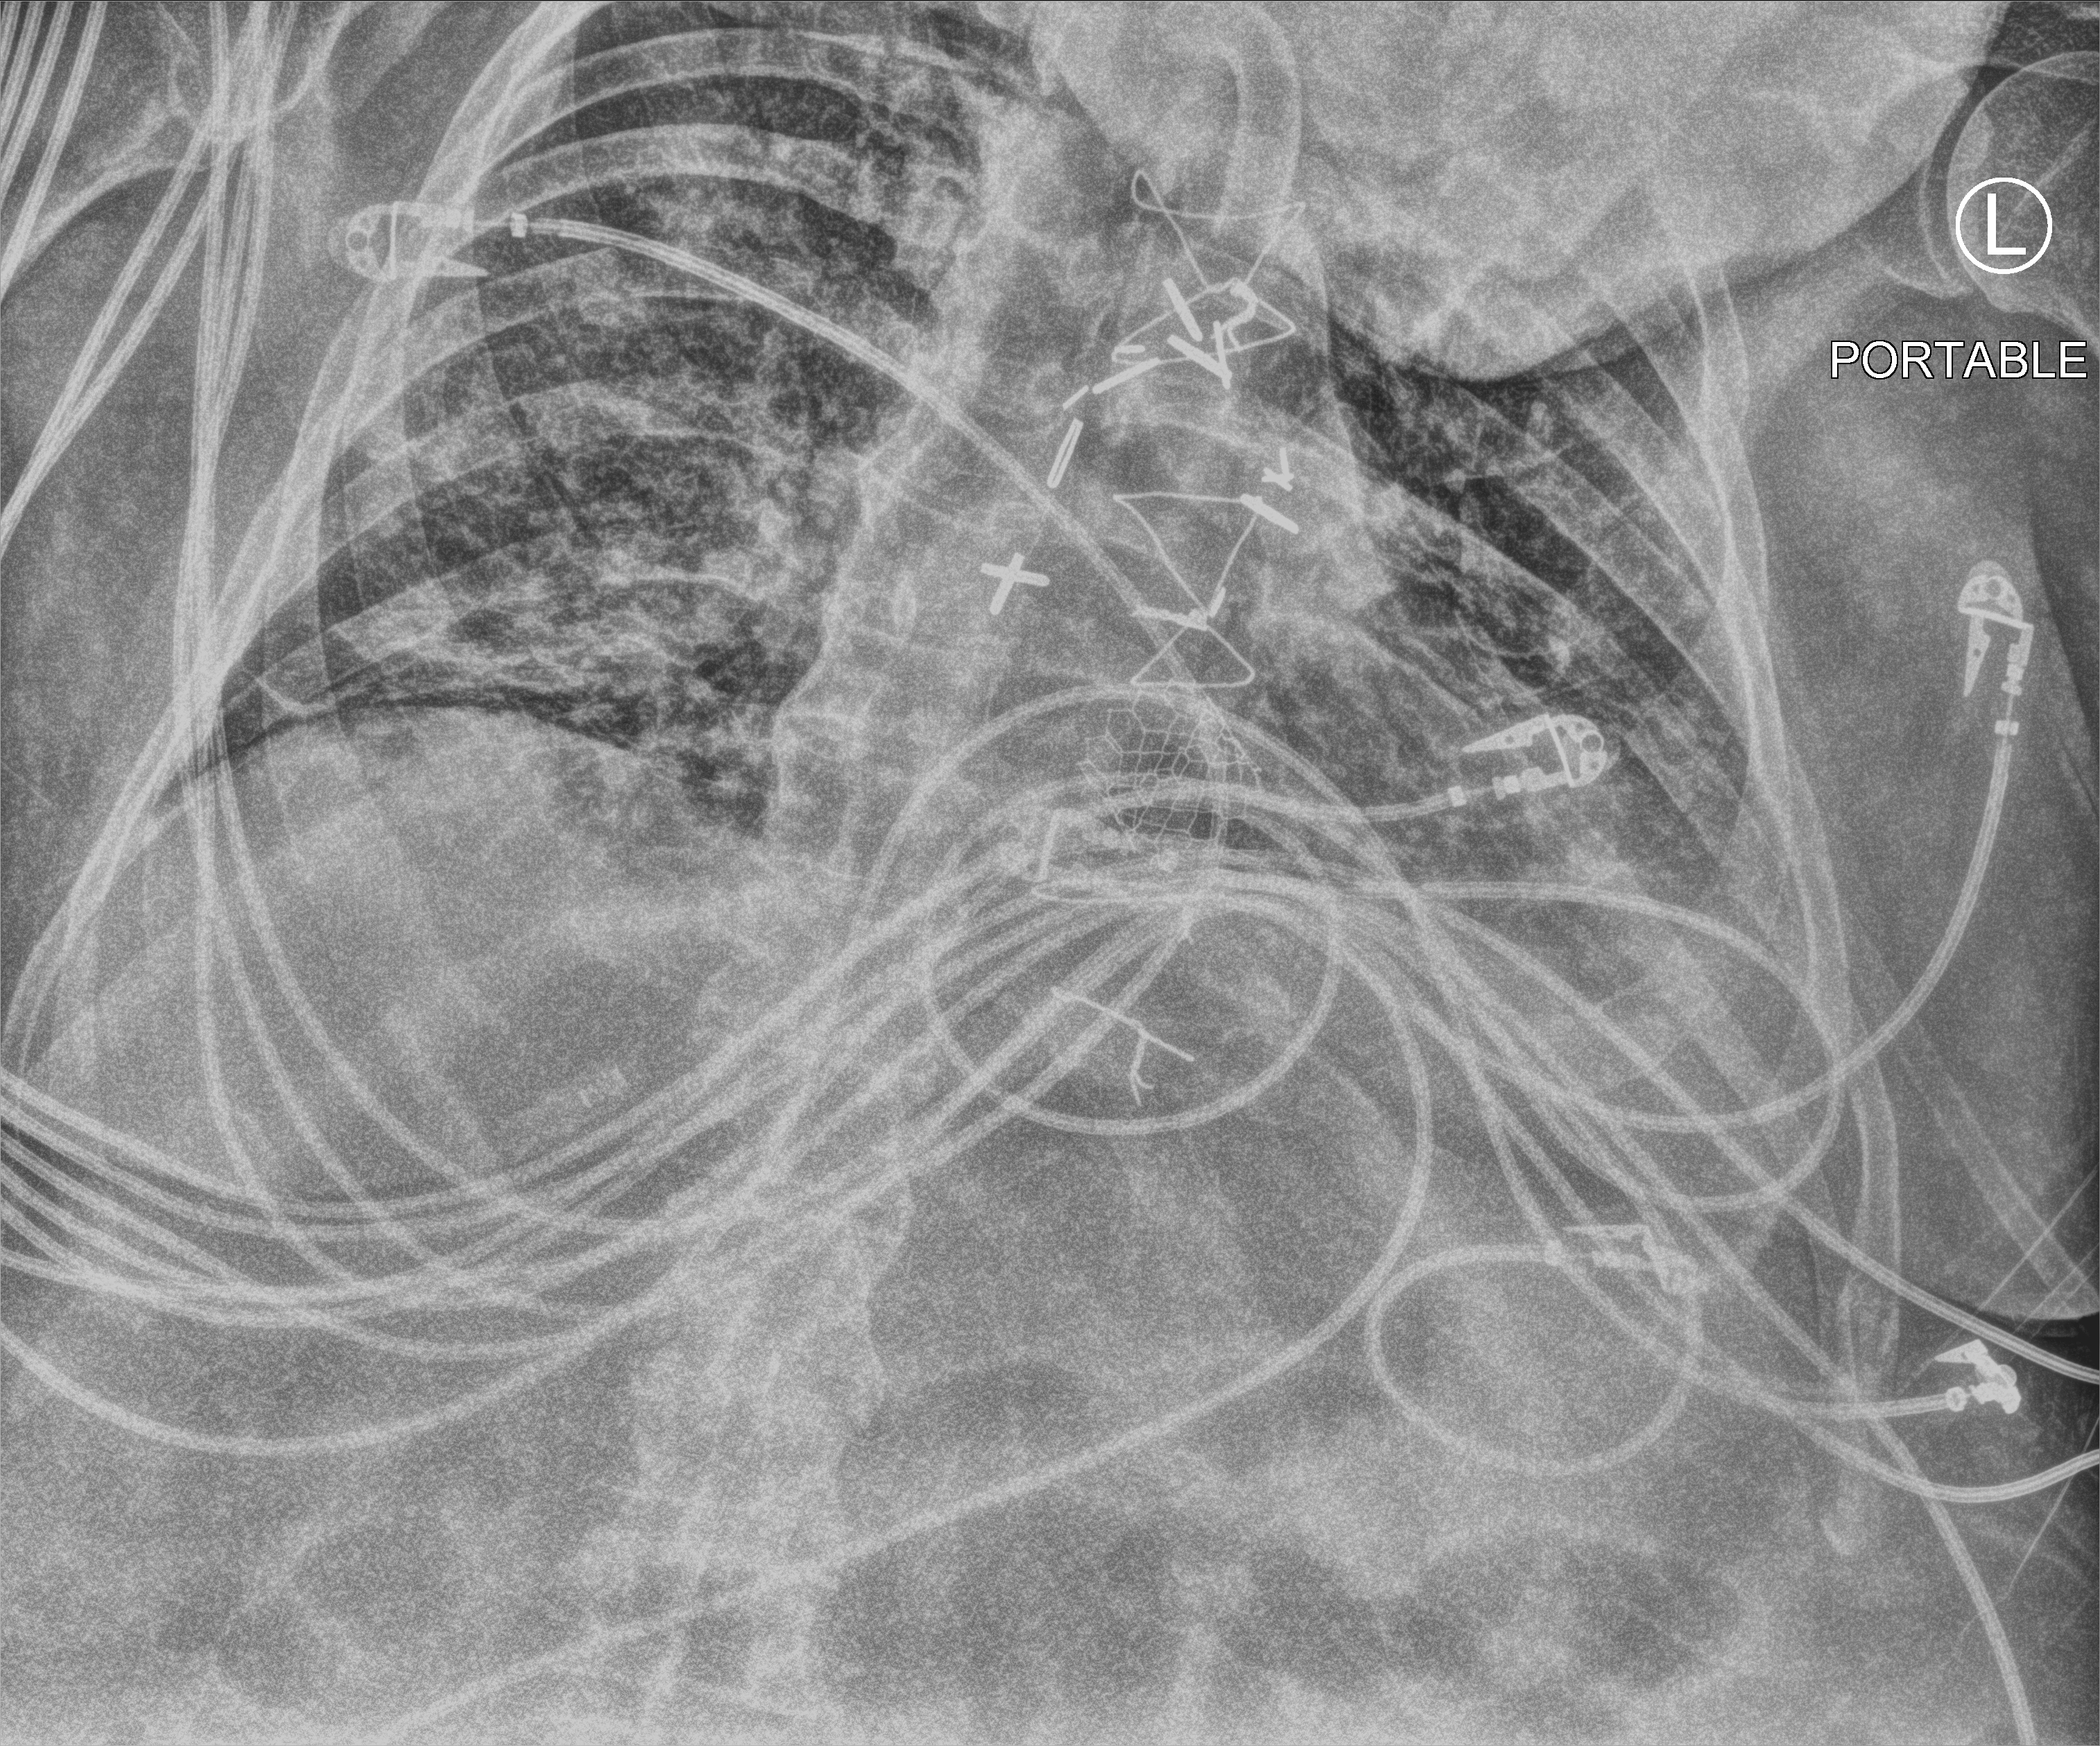
Portable chest radiograph, anteroposterior (AP) projection. Male patient hospitalised with COVID-19, age 60–74 years.
Hospital-stay facts (about this admission, not read from this image; timing relative to this image not recorded):
- diabetes (admission record): no
- mechanically ventilated during this hospital stay: yes
- hypertension (admission record): yes